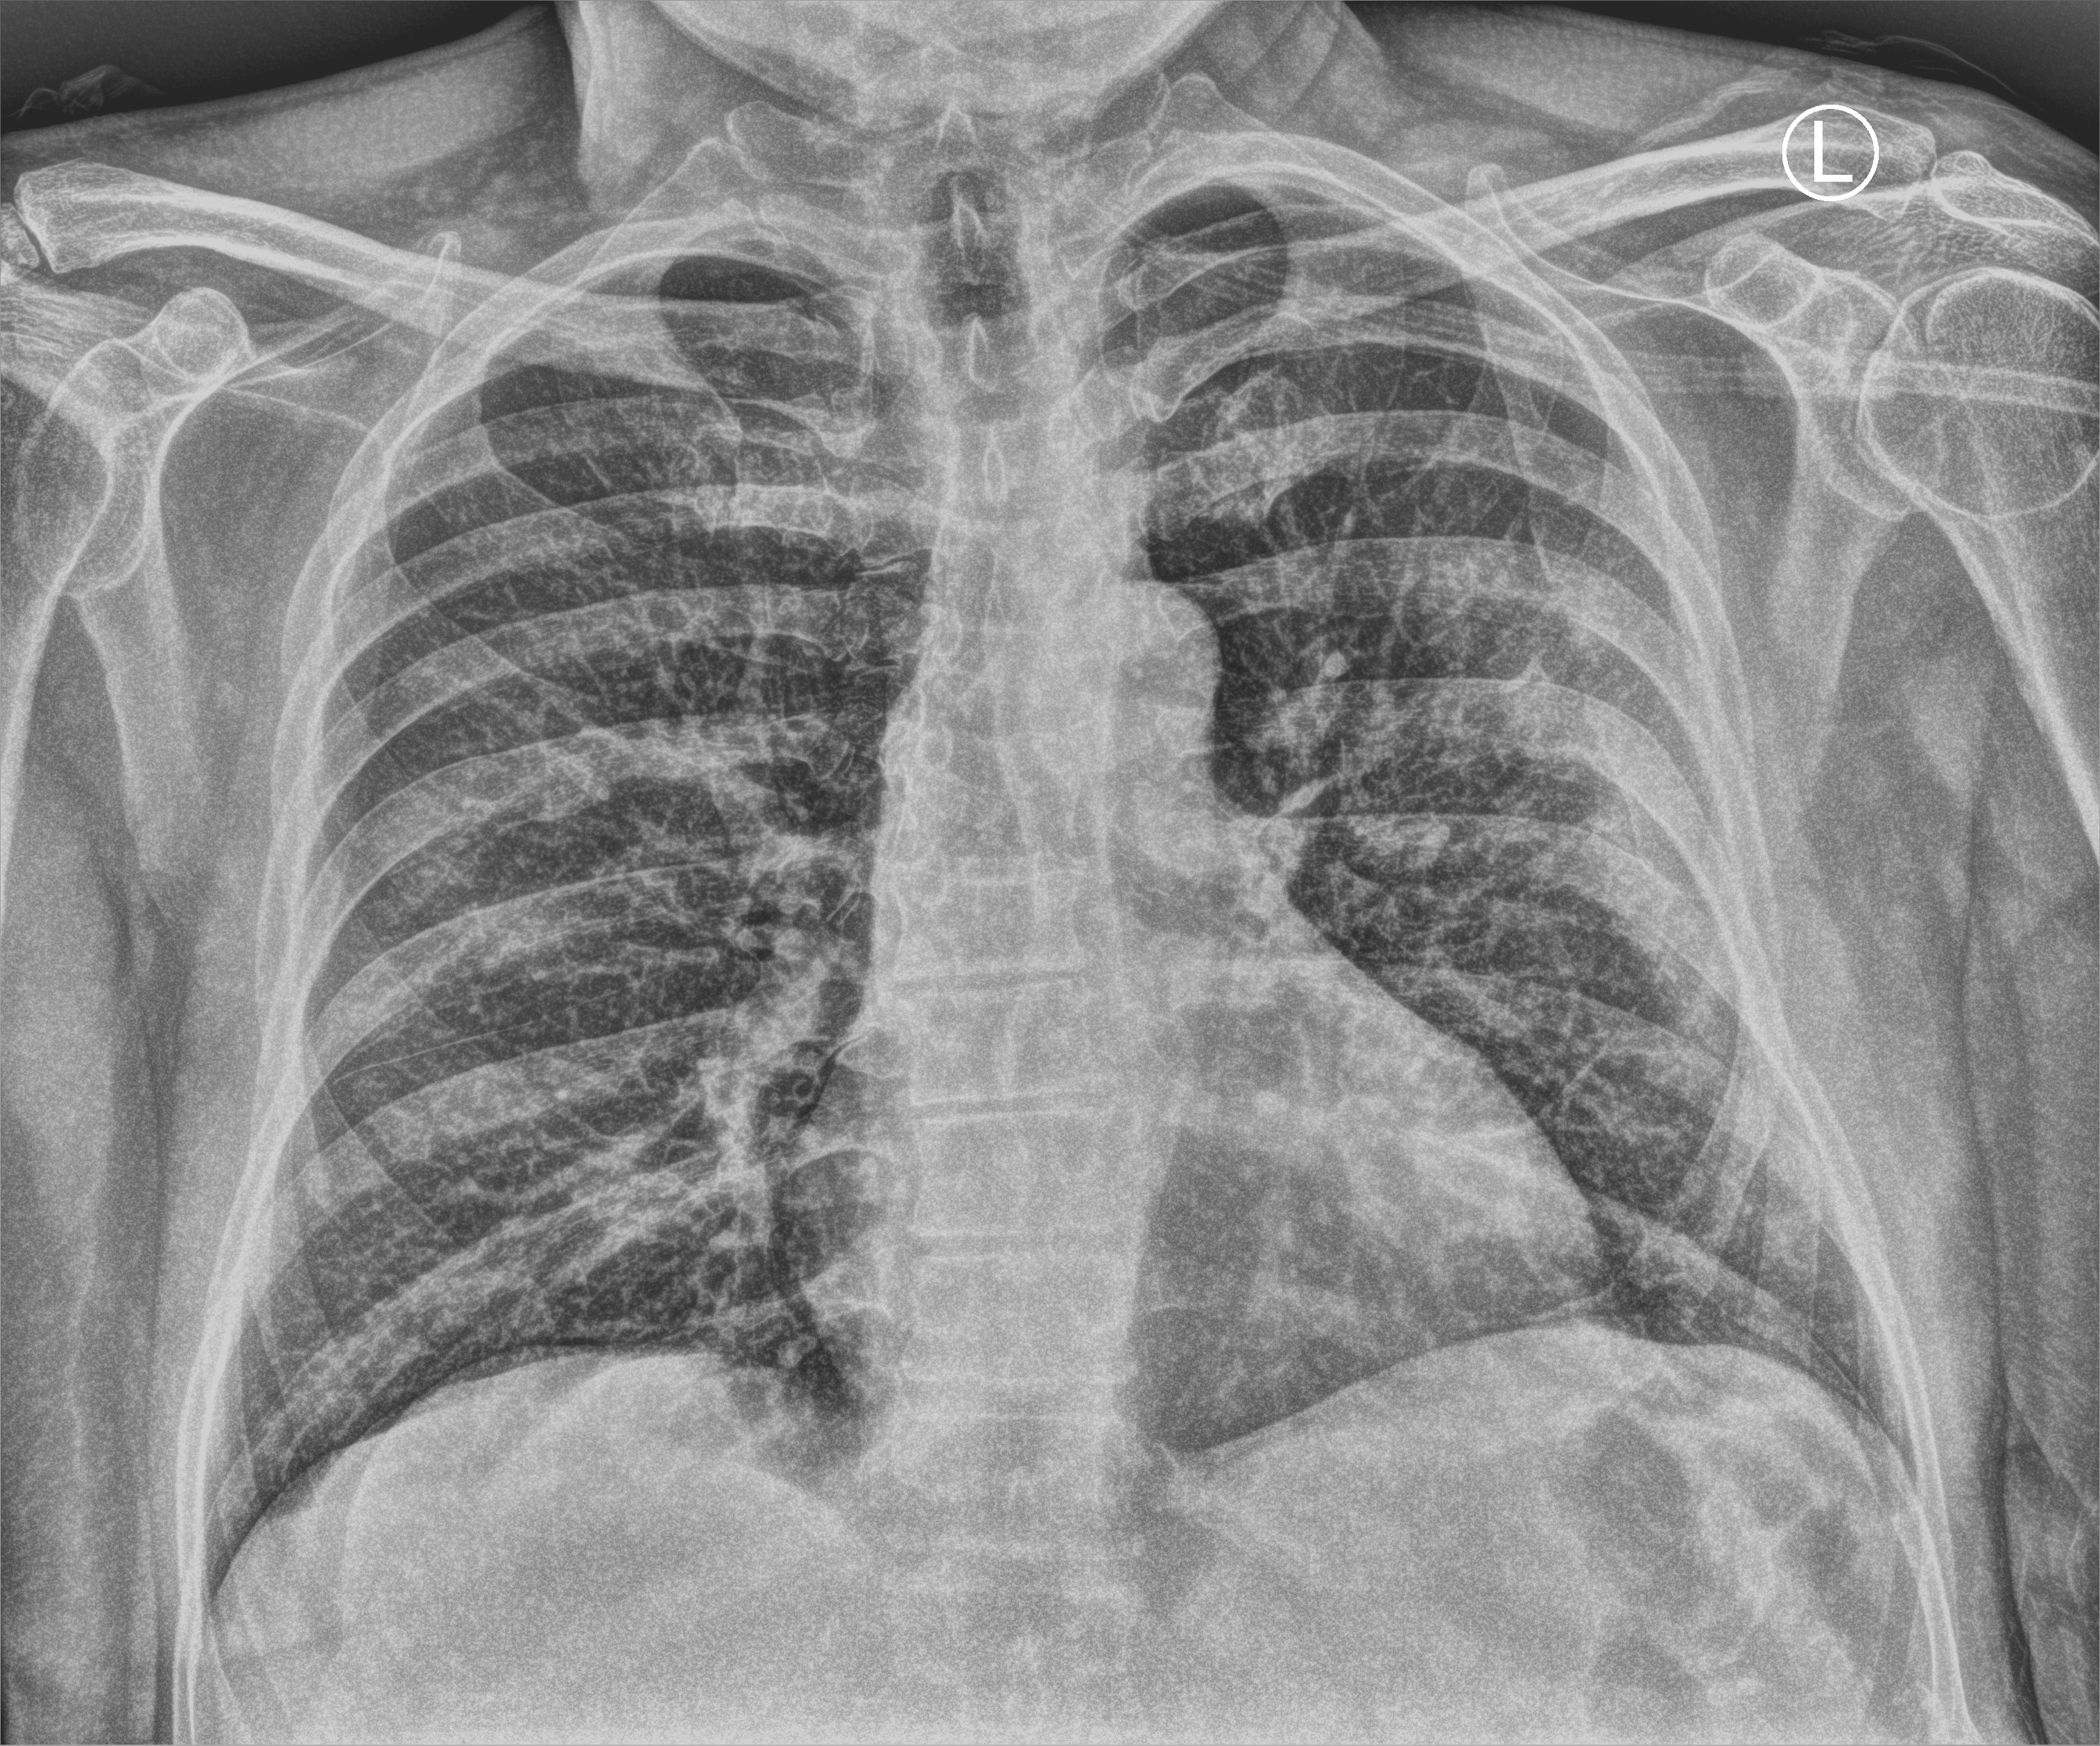
Bedside chest radiograph (computed radiography); anteroposterior (AP) projection. Male patient hospitalised with COVID-19, age 60–74 years.
Hospital-stay facts (about this admission, not read from this image; timing relative to this image not recorded):
- admitted to intensive care during this hospital stay: no
- diabetes (admission record): no
- mechanically ventilated during this hospital stay: no